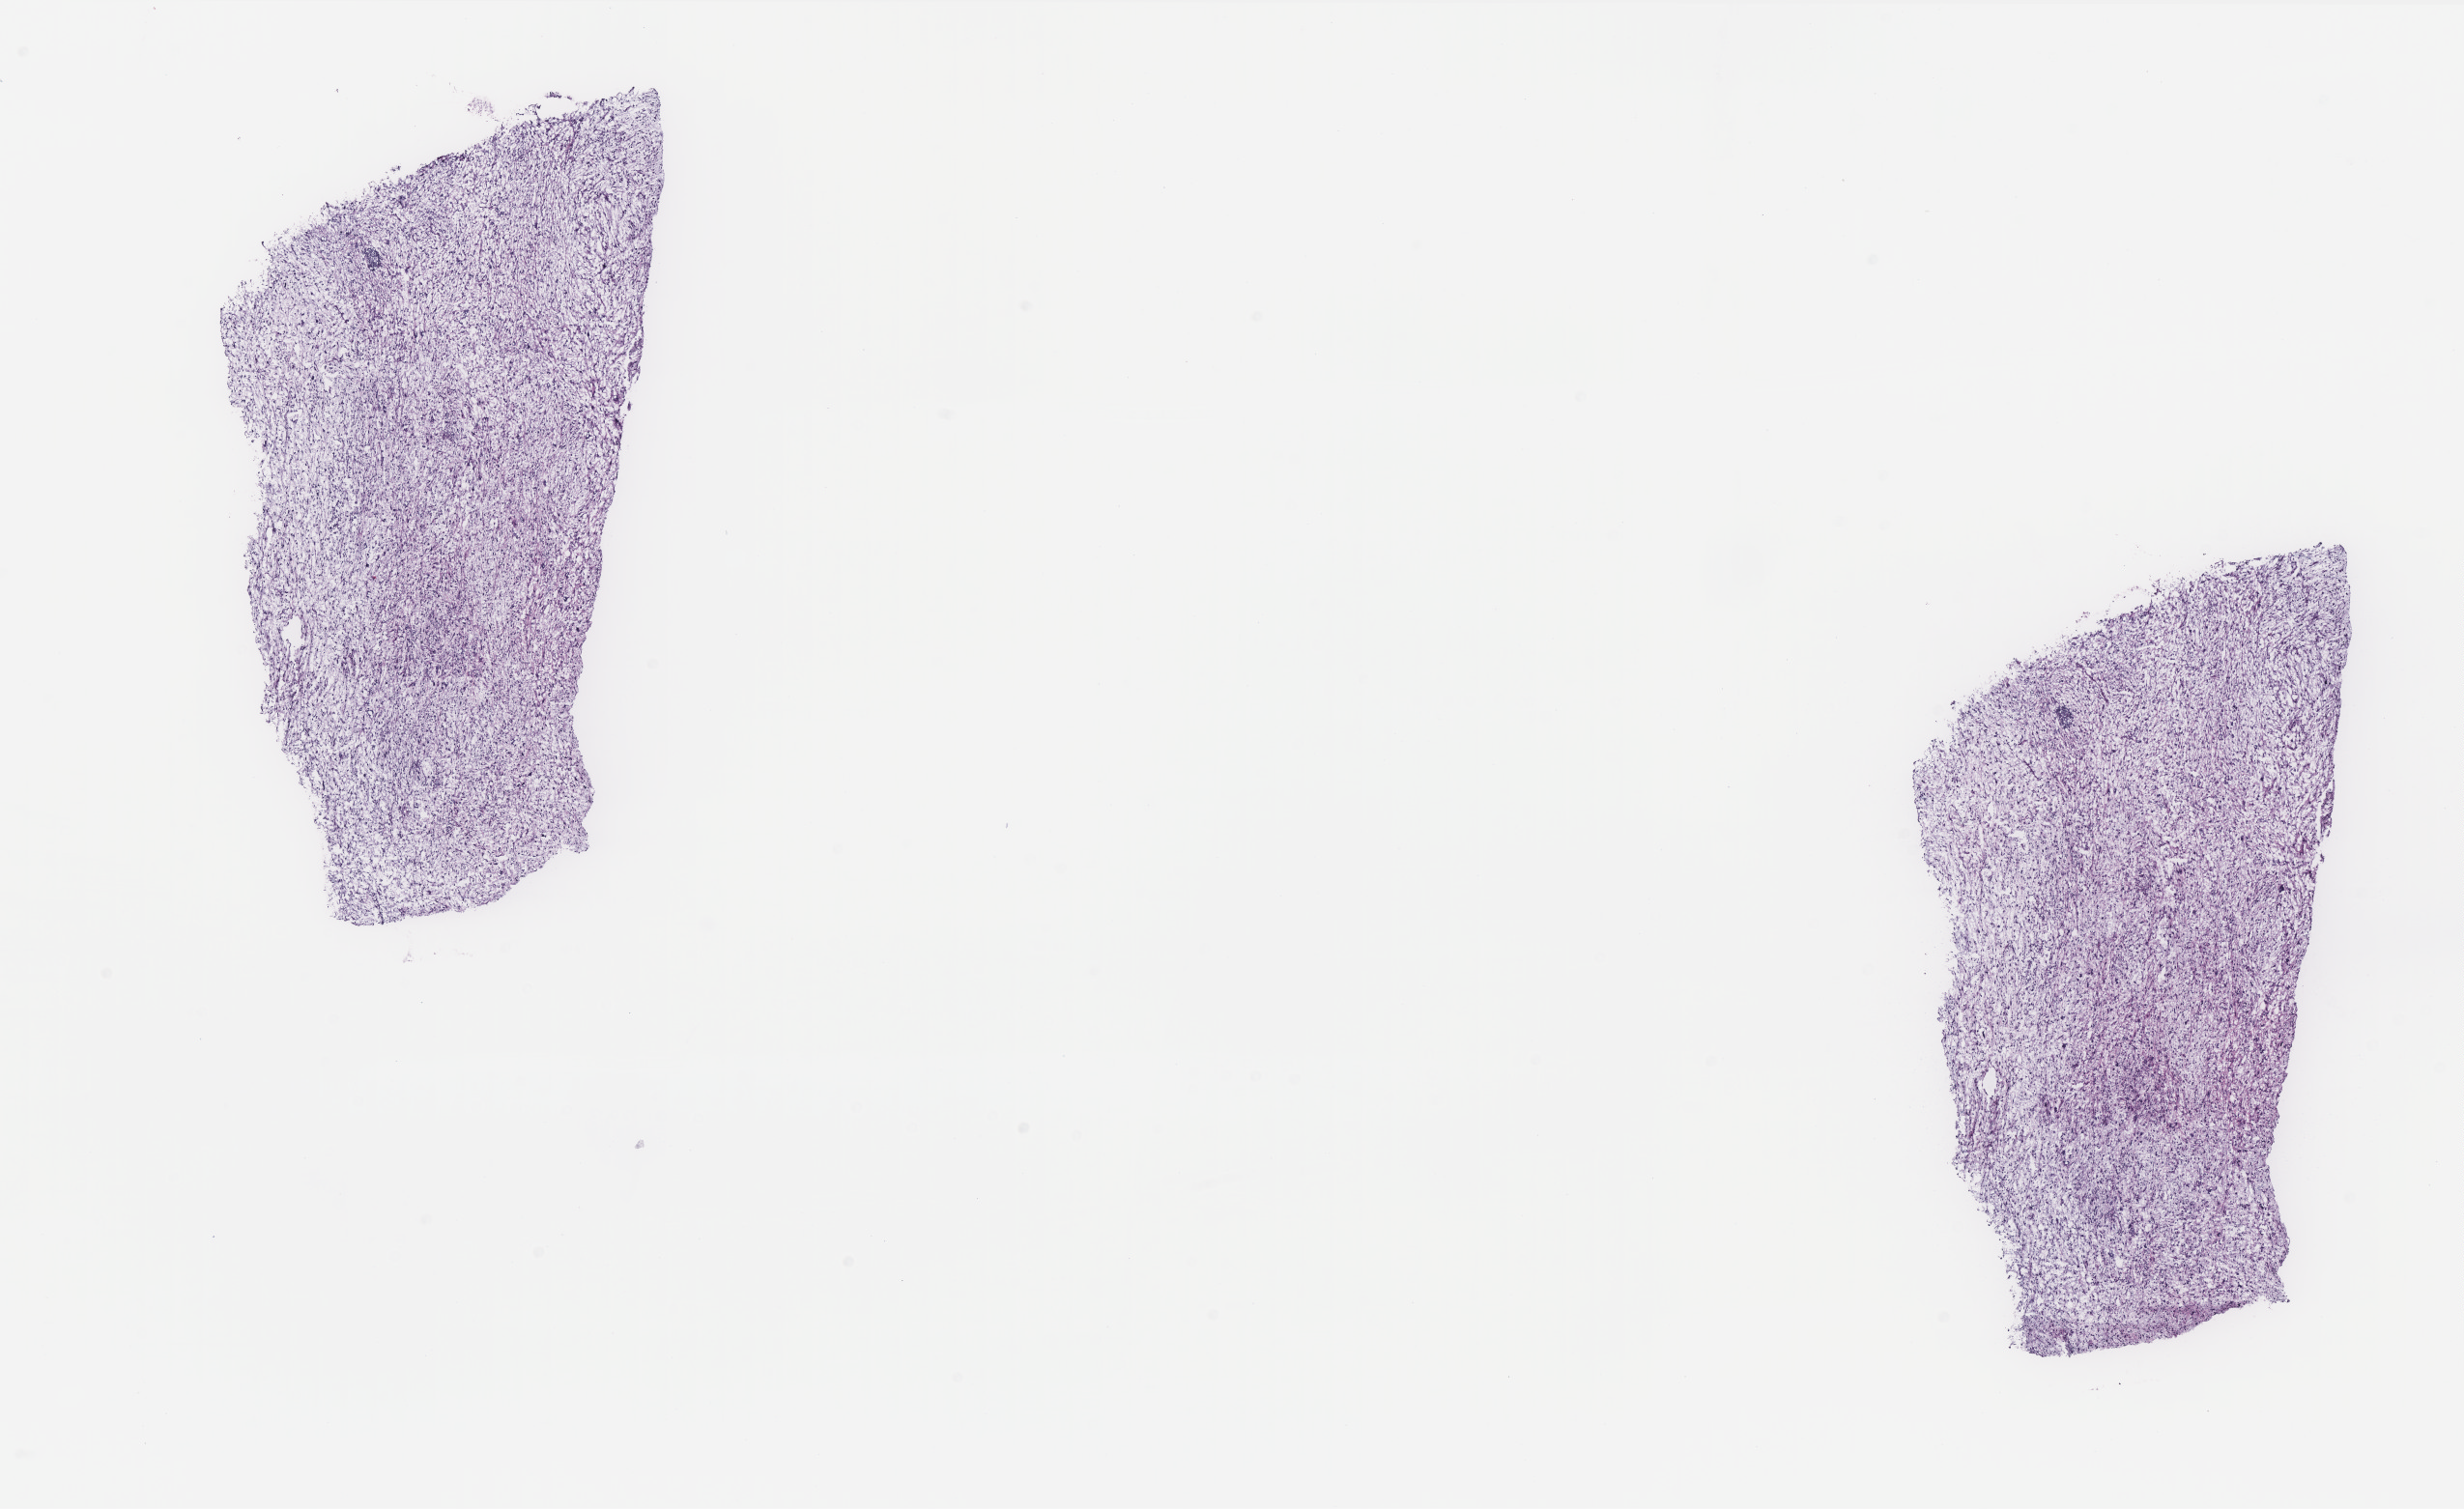
H&E-stained whole-slide image, low-resolution overview of the scanned area, about 20.4 x 12.5 mm (slide scanned at 40x), frozen section, primary tumour sample from the retroperitoneum and peritoneum. Patient: female, age at initial diagnosis 67 years. Slide review estimates, as recorded: tumour cells 90%, tumour nuclei 90%, normal cells 0%, stromal cells 10%, necrosis 0%. Inflammatory infiltration, as recorded: lymphocyte infiltration 2%, monocyte infiltration 1%, neutrophil infiltration 1%.
Diagnosis: Dedifferentiated liposarcoma (retroperitoneum).